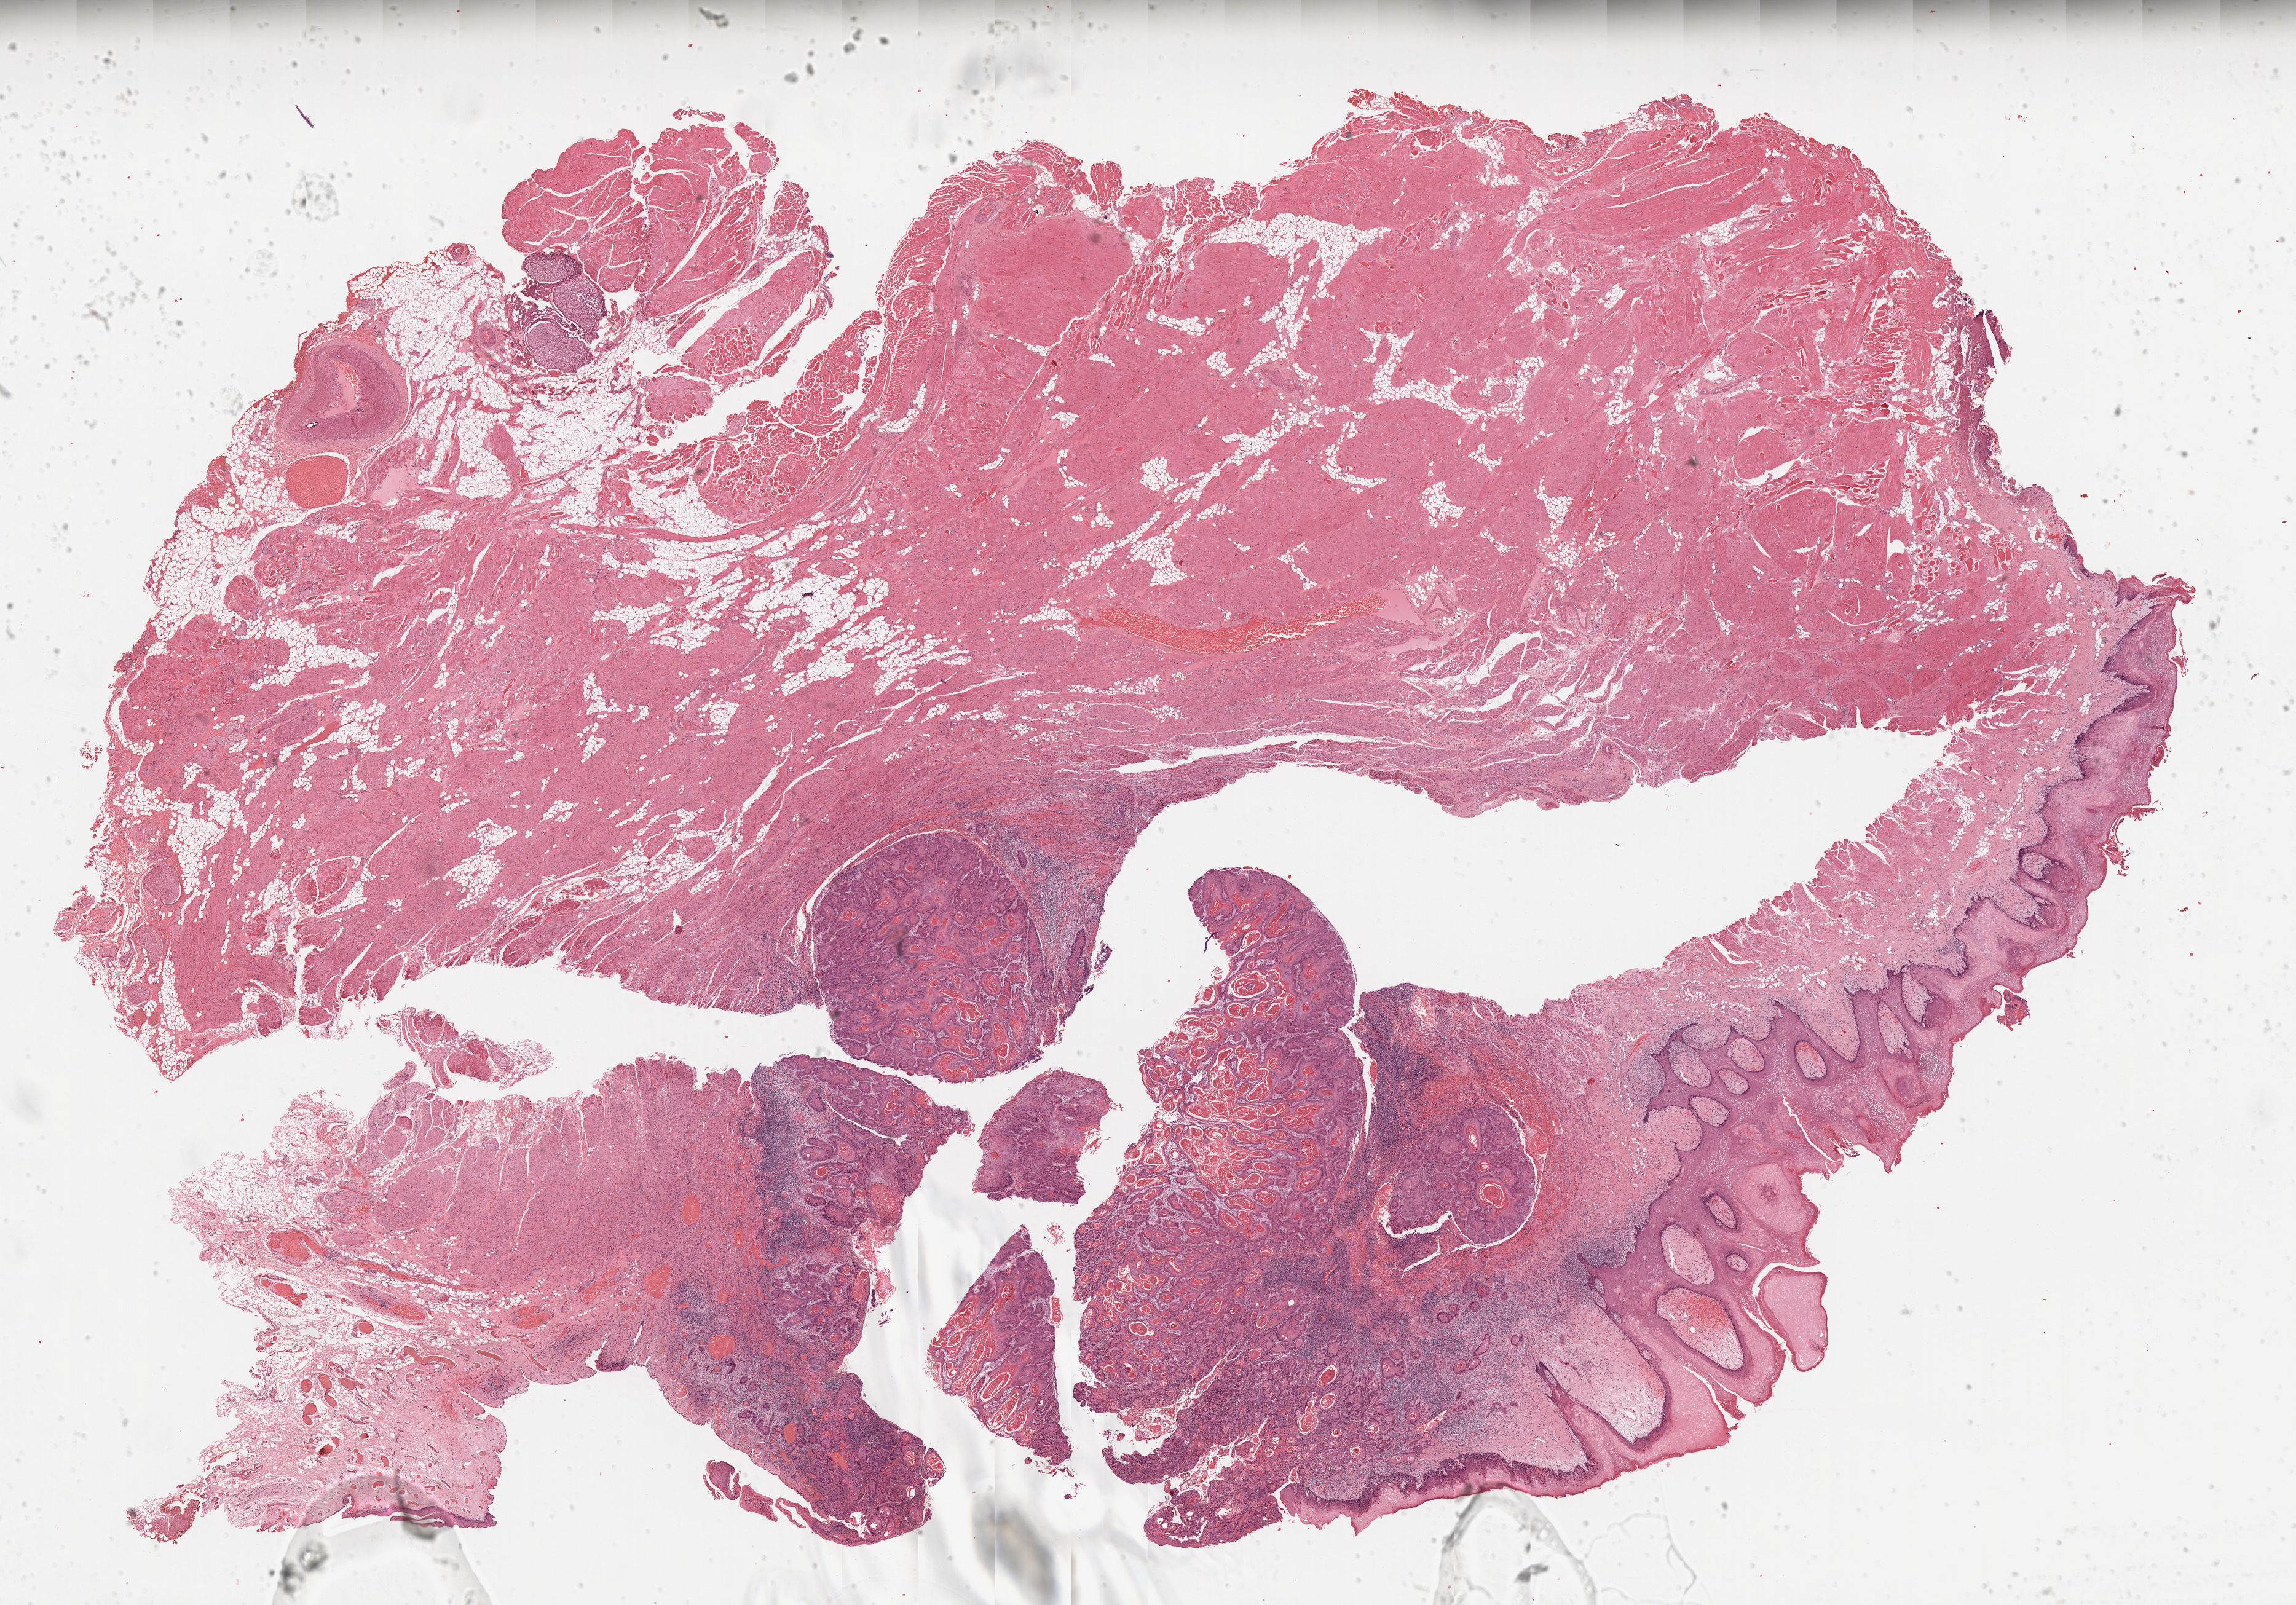
Whole-slide histology image, Hematoxylin and eosin (H&E) stained — shown as a low-resolution overview of the whole scanned area (about 30.0 x 20.9 mm, acquisition: 20x scan). Formalin-fixed paraffin-embedded (FFPE) diagnostic section. Head and neck, primary tumour sample. Patient: male, age at initial diagnosis 40 years.
Pathologic diagnosis: Squamous cell carcinoma, NOS (tongue, NOS).